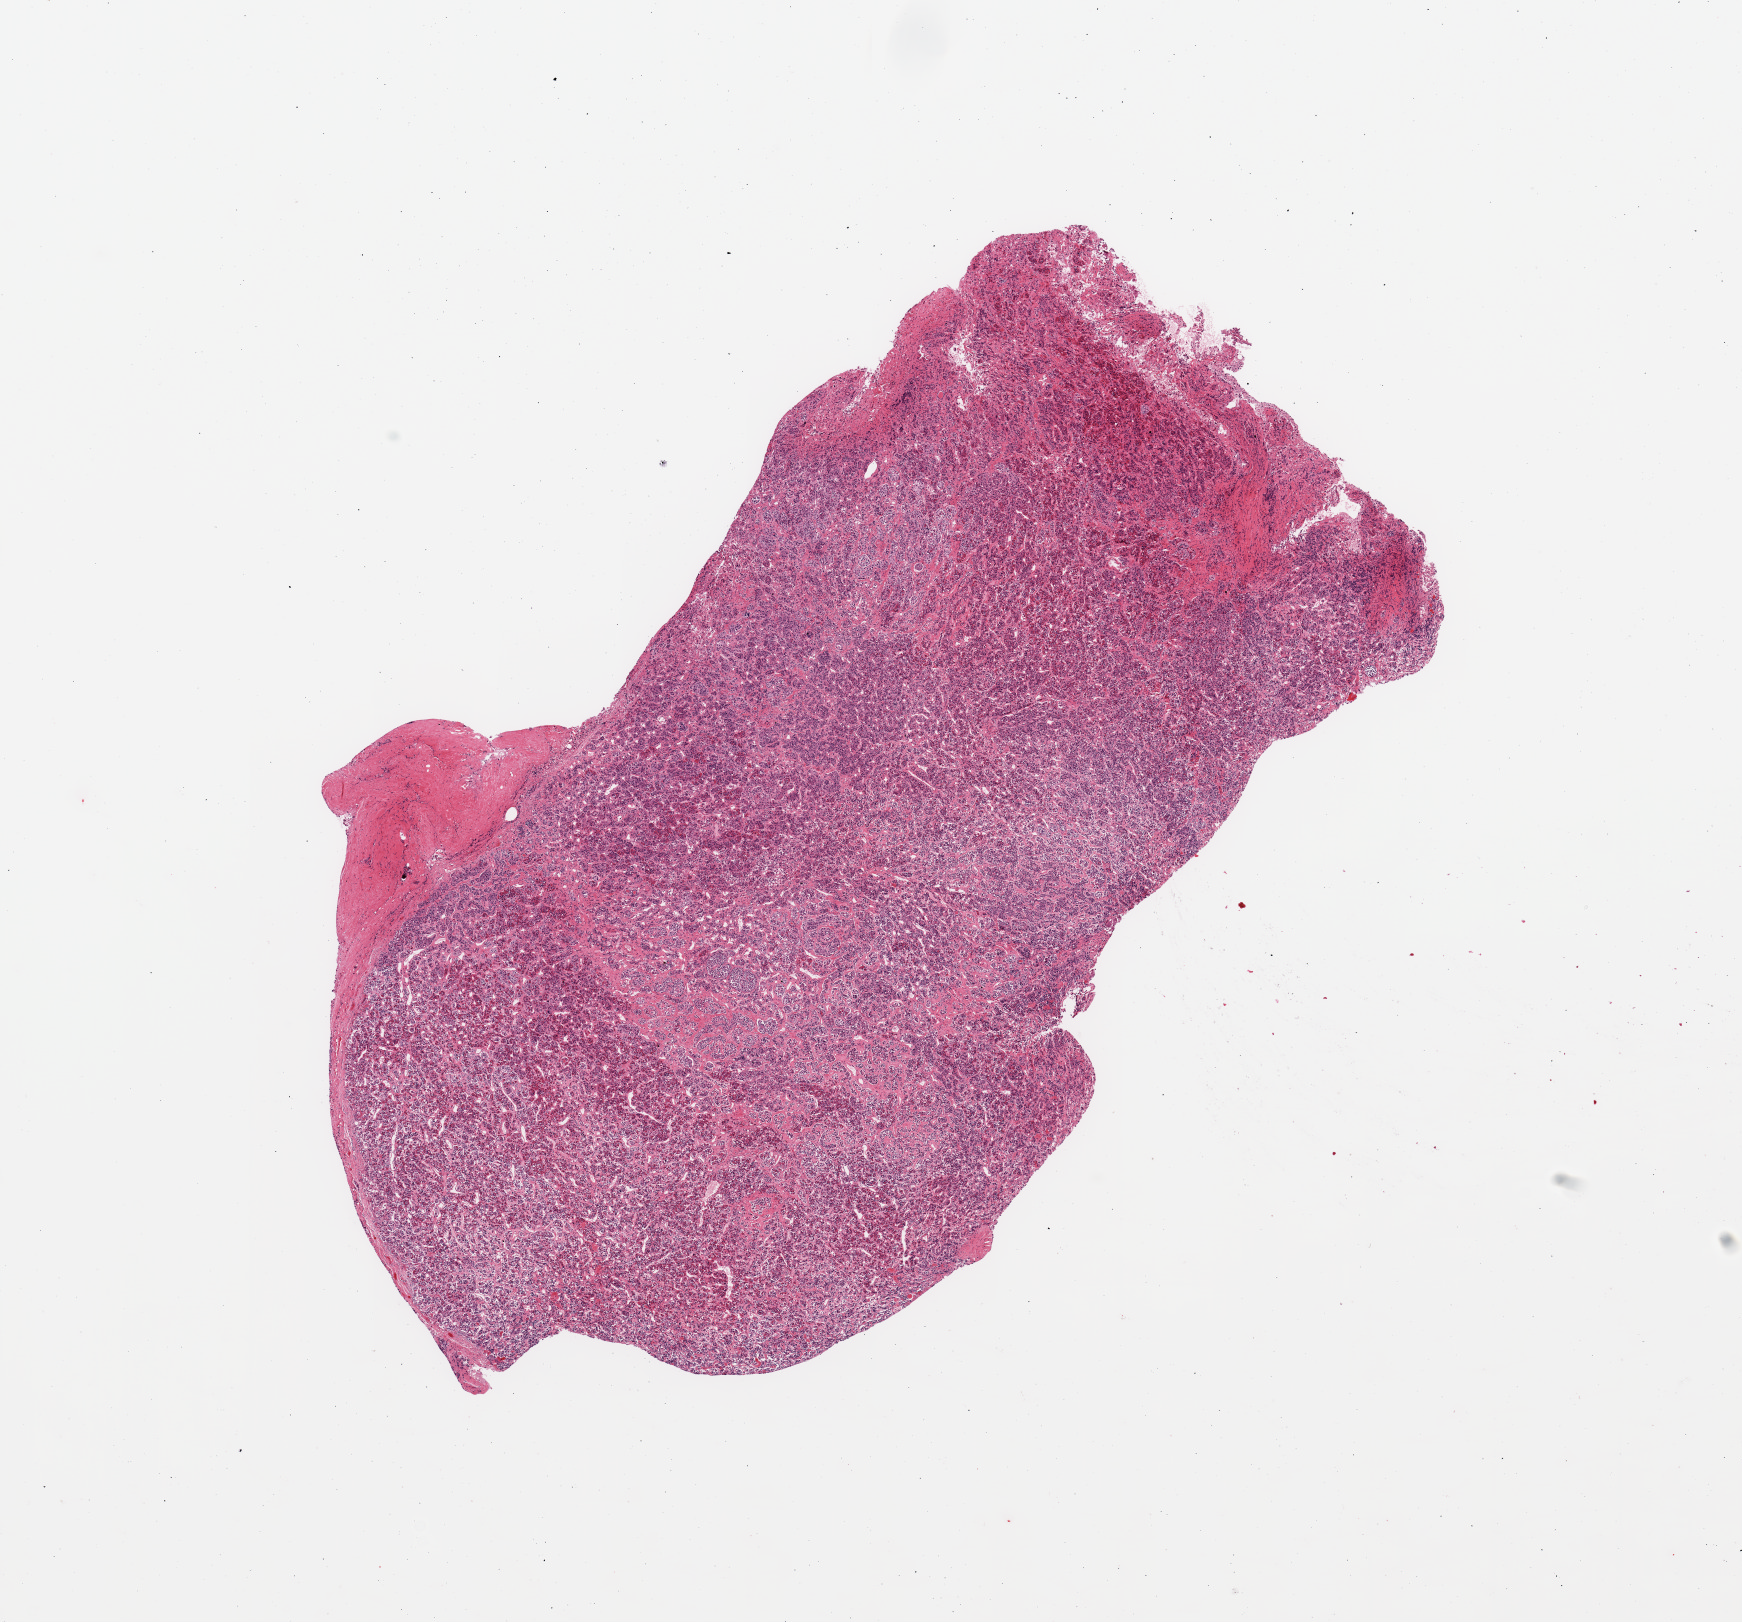
Digitized haematoxylin and eosin-stained section — a low-resolution overview of the entire scanned area, about 13.8 x 12.8 mm (from a 20x scan), PAXgene-fixed paraffin-embedded (PFPE) section, sampled site (target tissue): pituitary, donor tissue sample.
Pathologist's review note for this sample: 1 piece; all adenohypophysis.